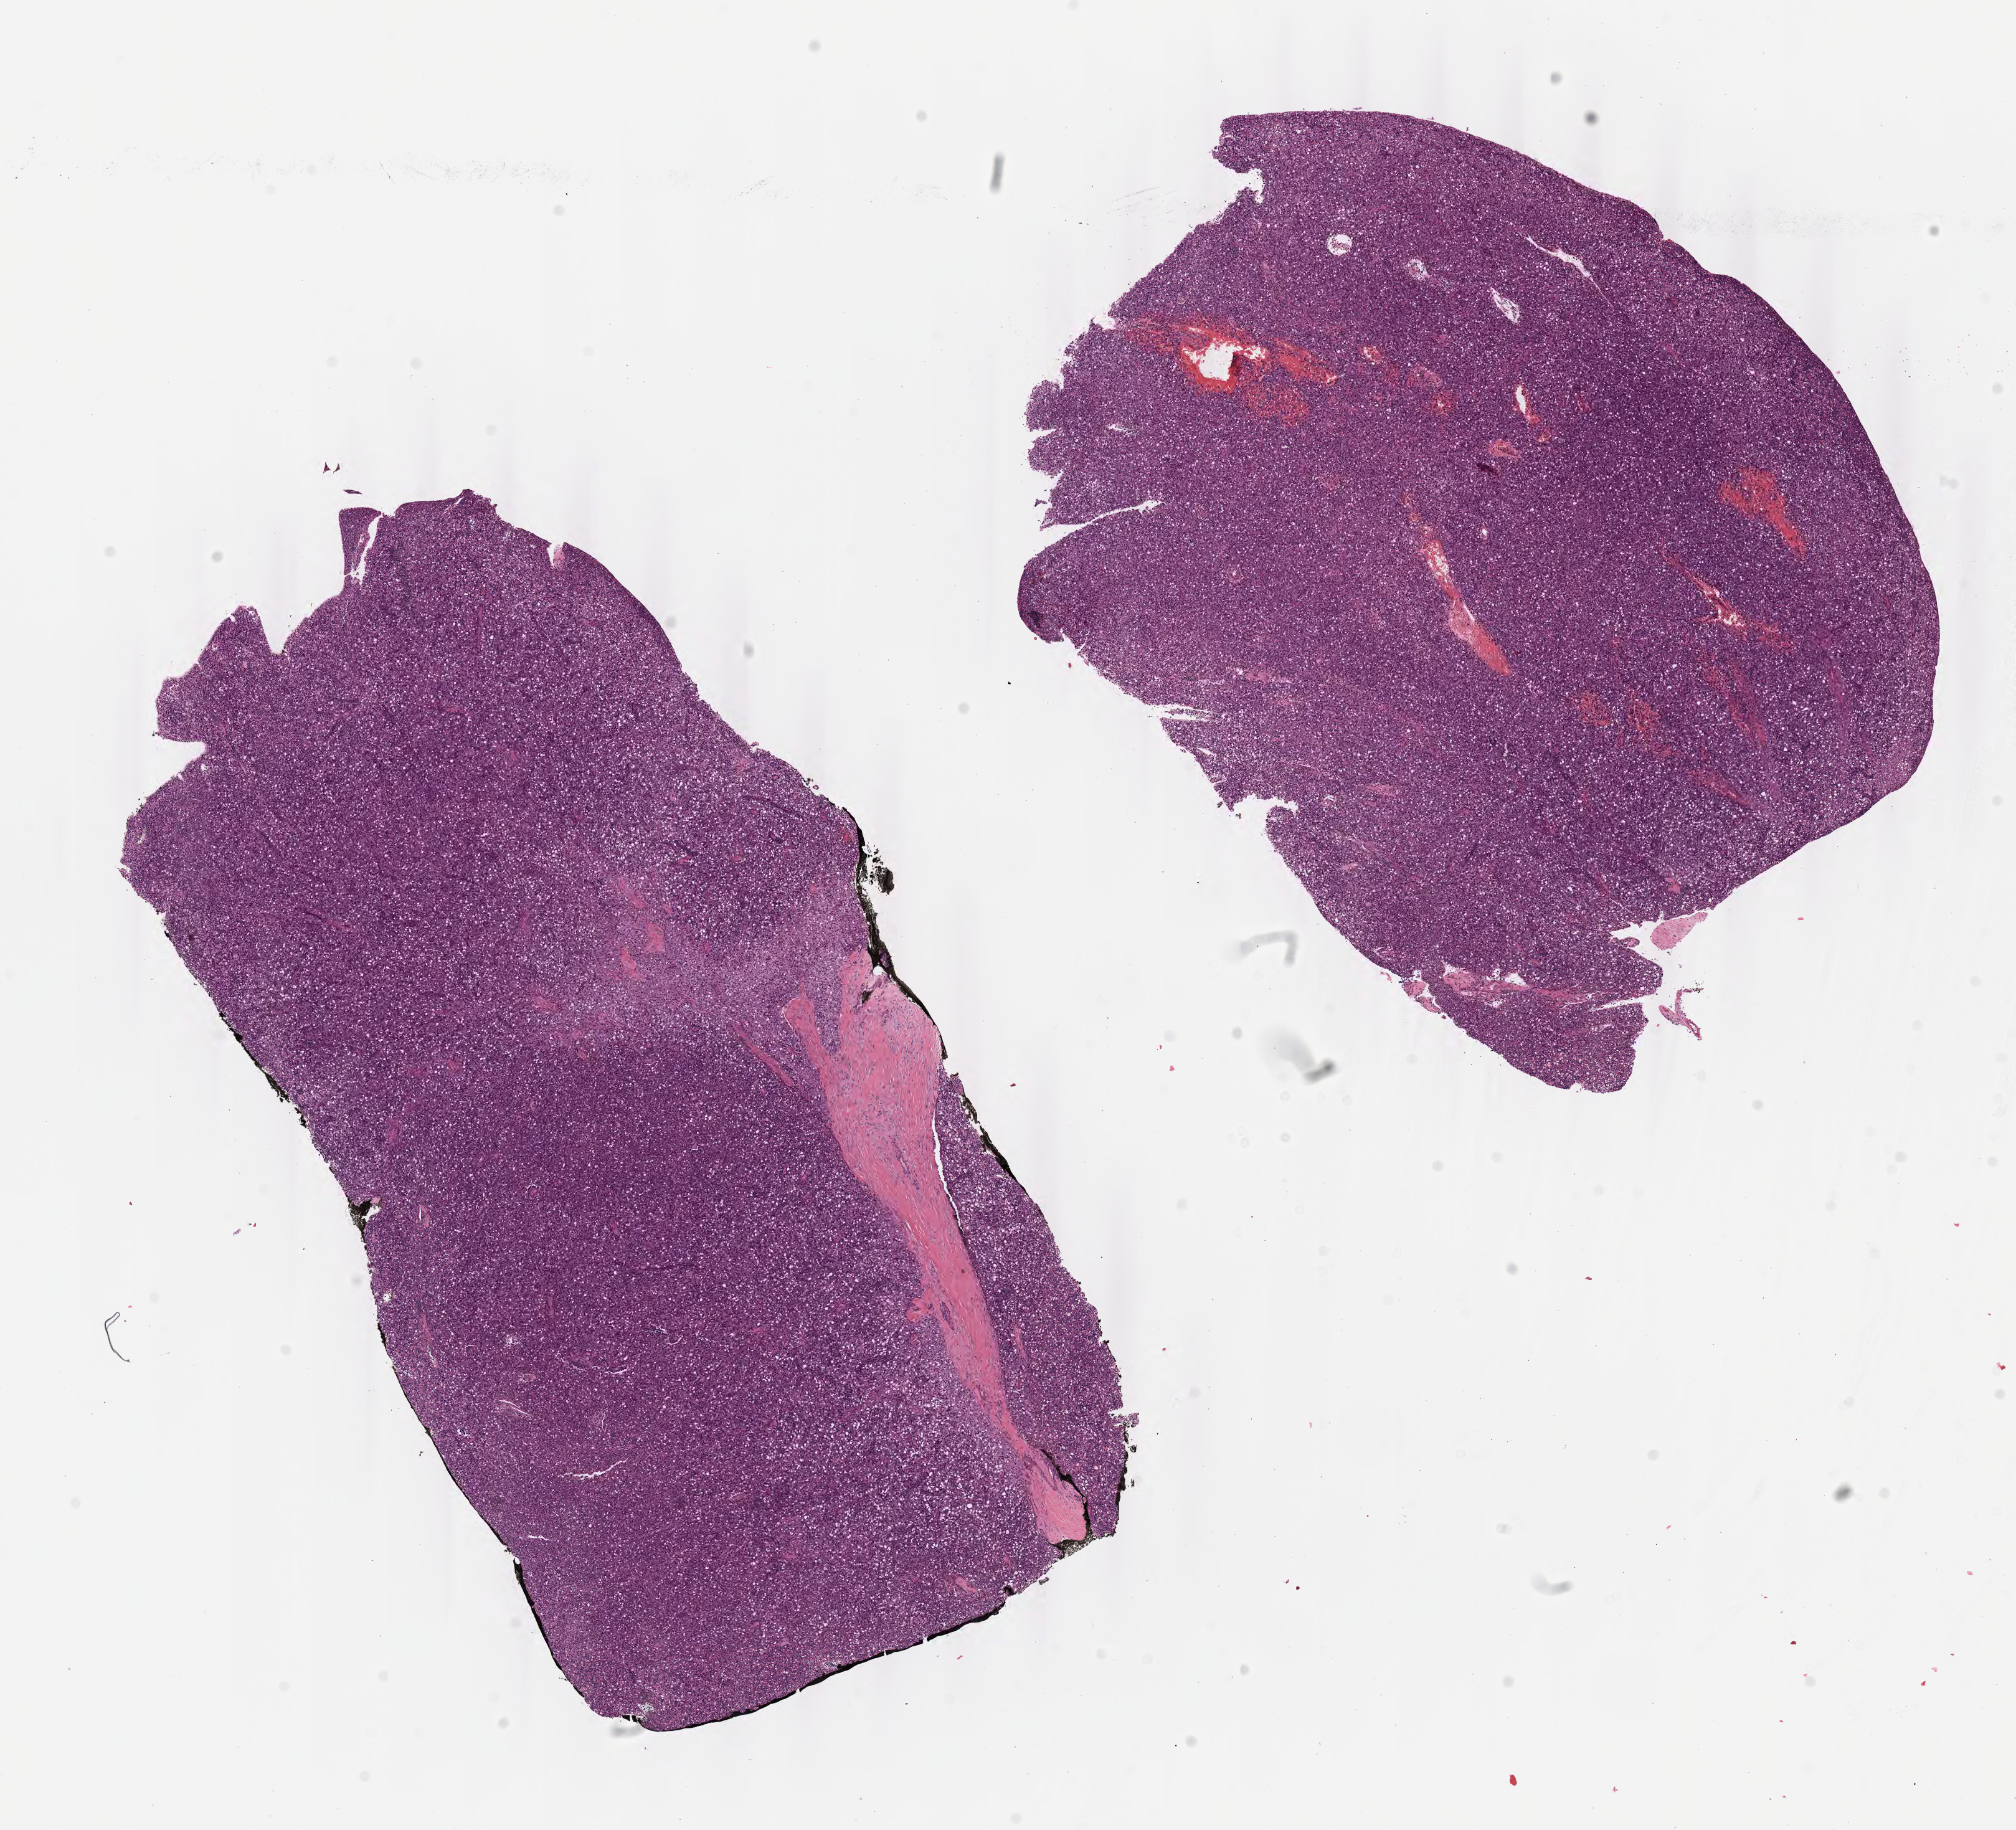
Whole-slide histology image, H&E-stained — whole scanned area (about 12.8 x 11.6 mm, slide scanned at 40x) shown as a low-resolution overview, FFPE section, primary tumour sample from the thymus. Patient: female, age at initial diagnosis 71 years.
Histologic diagnosis: Thymoma, type B3, malignant.